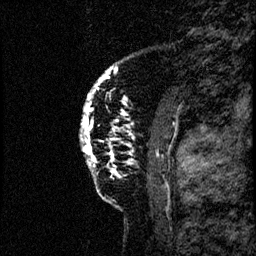
Breast MRI (dynamic contrast-enhanced), one sagittal slice. Position 13 of 60 along the scan axis. Dynamic contrast-enhanced study with each time point stored as its own series, time point 2 of 4 at this slice position (early post-contrast, ordered by acquisition time). 1.5 T. TE 4.2 ms, TR 17.6 ms. 2 mm slice thickness. 256 × 256 image matrix, field of view 200 × 200 mm. Female patient, age 40 years. From the clinical record (not read from this slice): setting: breast cancer imaged before/during neoadjuvant chemotherapy; receptor status: HER2-positive.
Structures marked on this image (semi-automatically segmented with operator editing):
- analysis volume of interest (the breast-tissue region the enhancement analysis was run in; not a lesion): box from (x=76, y=55) to (x=183, y=206) px
- tumour enhancement mask (voxels above the 100 % enhancement threshold inside the analysis volume of interest): (x=80, y=66)–(x=113, y=165)